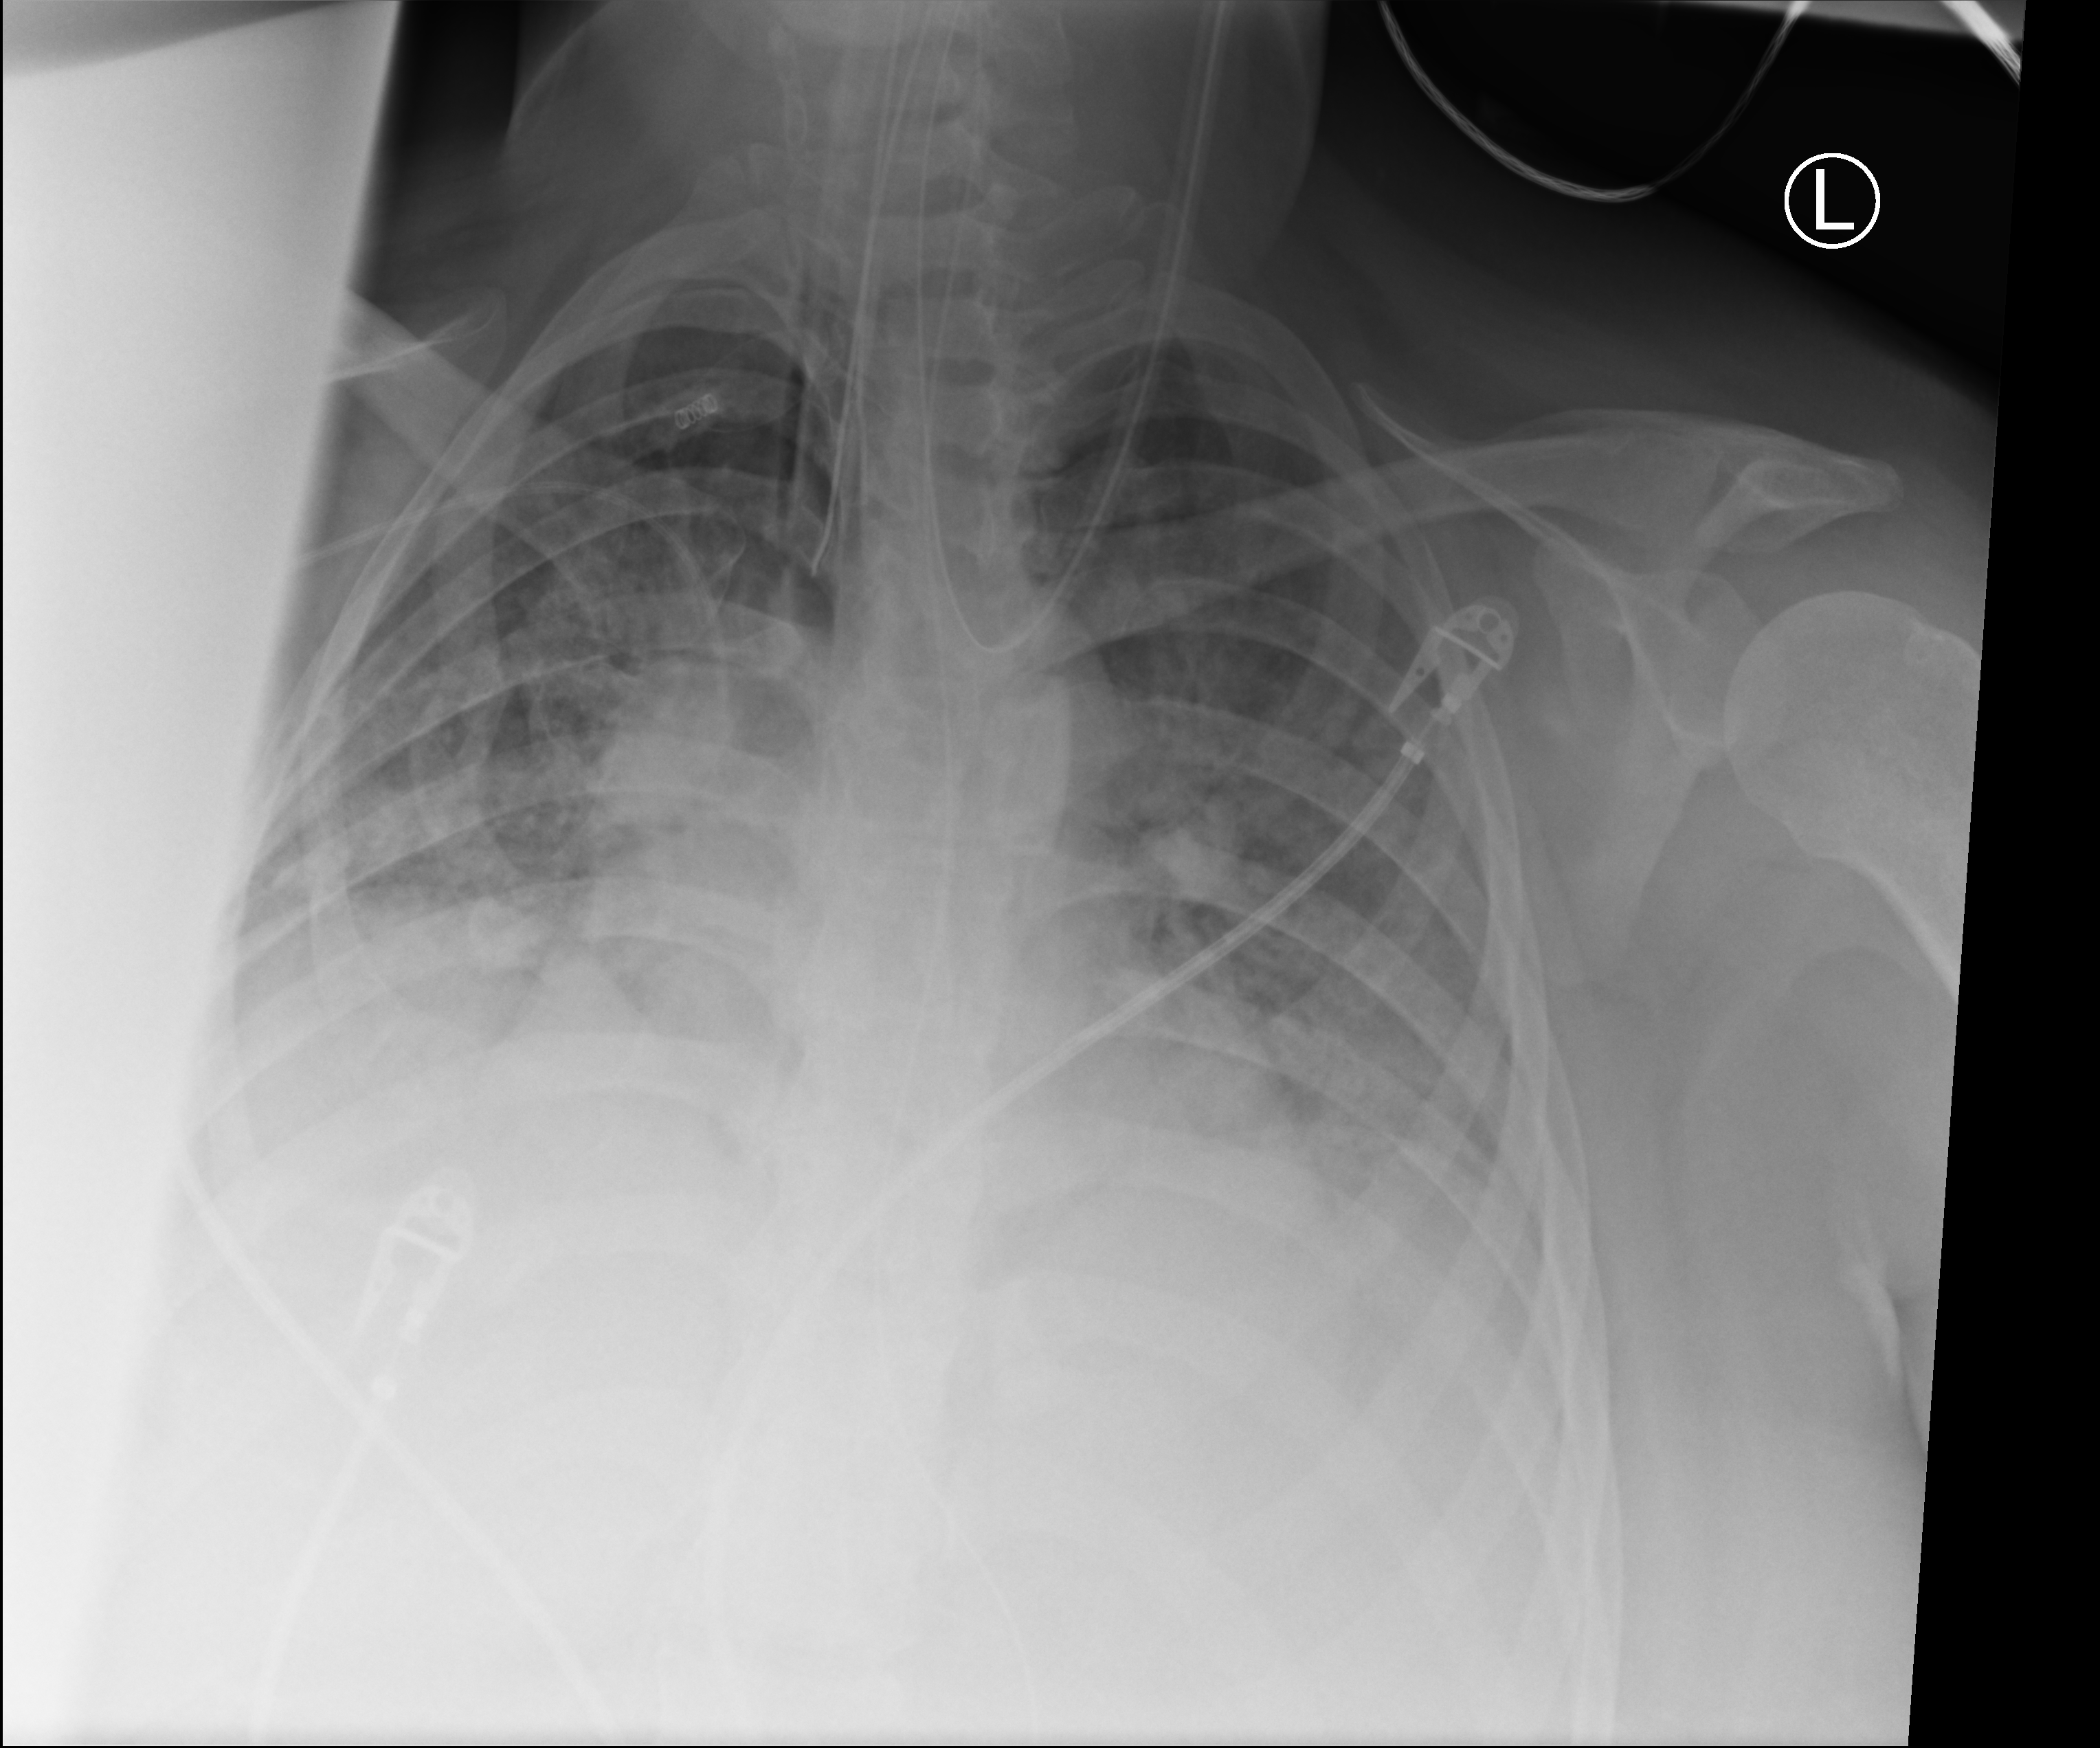
Portable chest radiograph, anteroposterior (AP) projection. Patient hospitalised with COVID-19; female, aged 18–59 years.
Admission-level facts for this patient (not findings on this image; timing relative to this image not recorded):
- admitted to intensive care during this hospital stay: yes